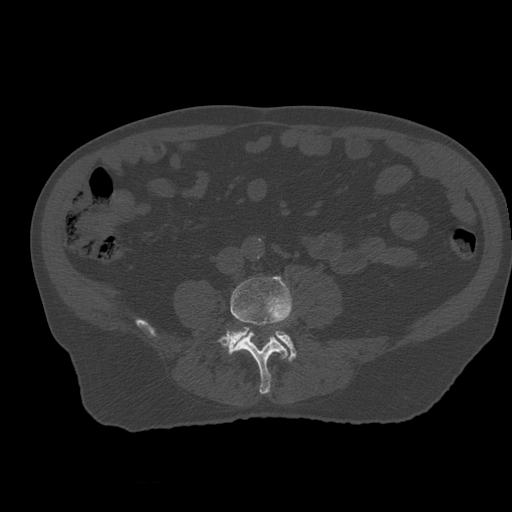
CT including the spine, one axial slice. Slice 159 of 399 in the series (ordered by position). Bone window (W 1800 / L 400 HU). 512 × 512 image matrix, field of view 407 × 407 mm. Patient age 73 years. From the clinical record (not read from this slice): primary cancer: prostate; vertebrae with lytic lesions (as recorded): L2.
Annotated regions visible in this slice (semi-automatic segmentation, software-assisted and operator-edited):
- L4 vertebra: bounding box <217,277,293,394> (left, top, right, bottom; pixels)
- L5 vertebra: <229,327,296,361>